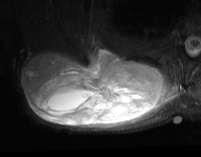
MRI of an extremity soft-tissue mass, one axial slice; slice 35 of 74 in the series (ordered by position); STIR; MR volume resampled by the dataset authors to the PET/CT grid (not the native acquisition matrix); 3.27 mm slice thickness; 201 × 157 image matrix, field of view 196 × 153 mm. Male patient. Case-level facts recorded for this patient, not image findings: histological type: pleiomorphic spindle cell undifferentiated; grade: high; site of the primary tumour: right parascapusular.
Outlined on this slice (expert contour drawn on MRI and transferred to this co-registered scan by the dataset authors):
- gross tumour volume including surrounding oedema: bounding box [x1, y1, x2, y2] px = [23, 48, 180, 129]
- gross tumour volume (mass): [23, 48, 166, 126]